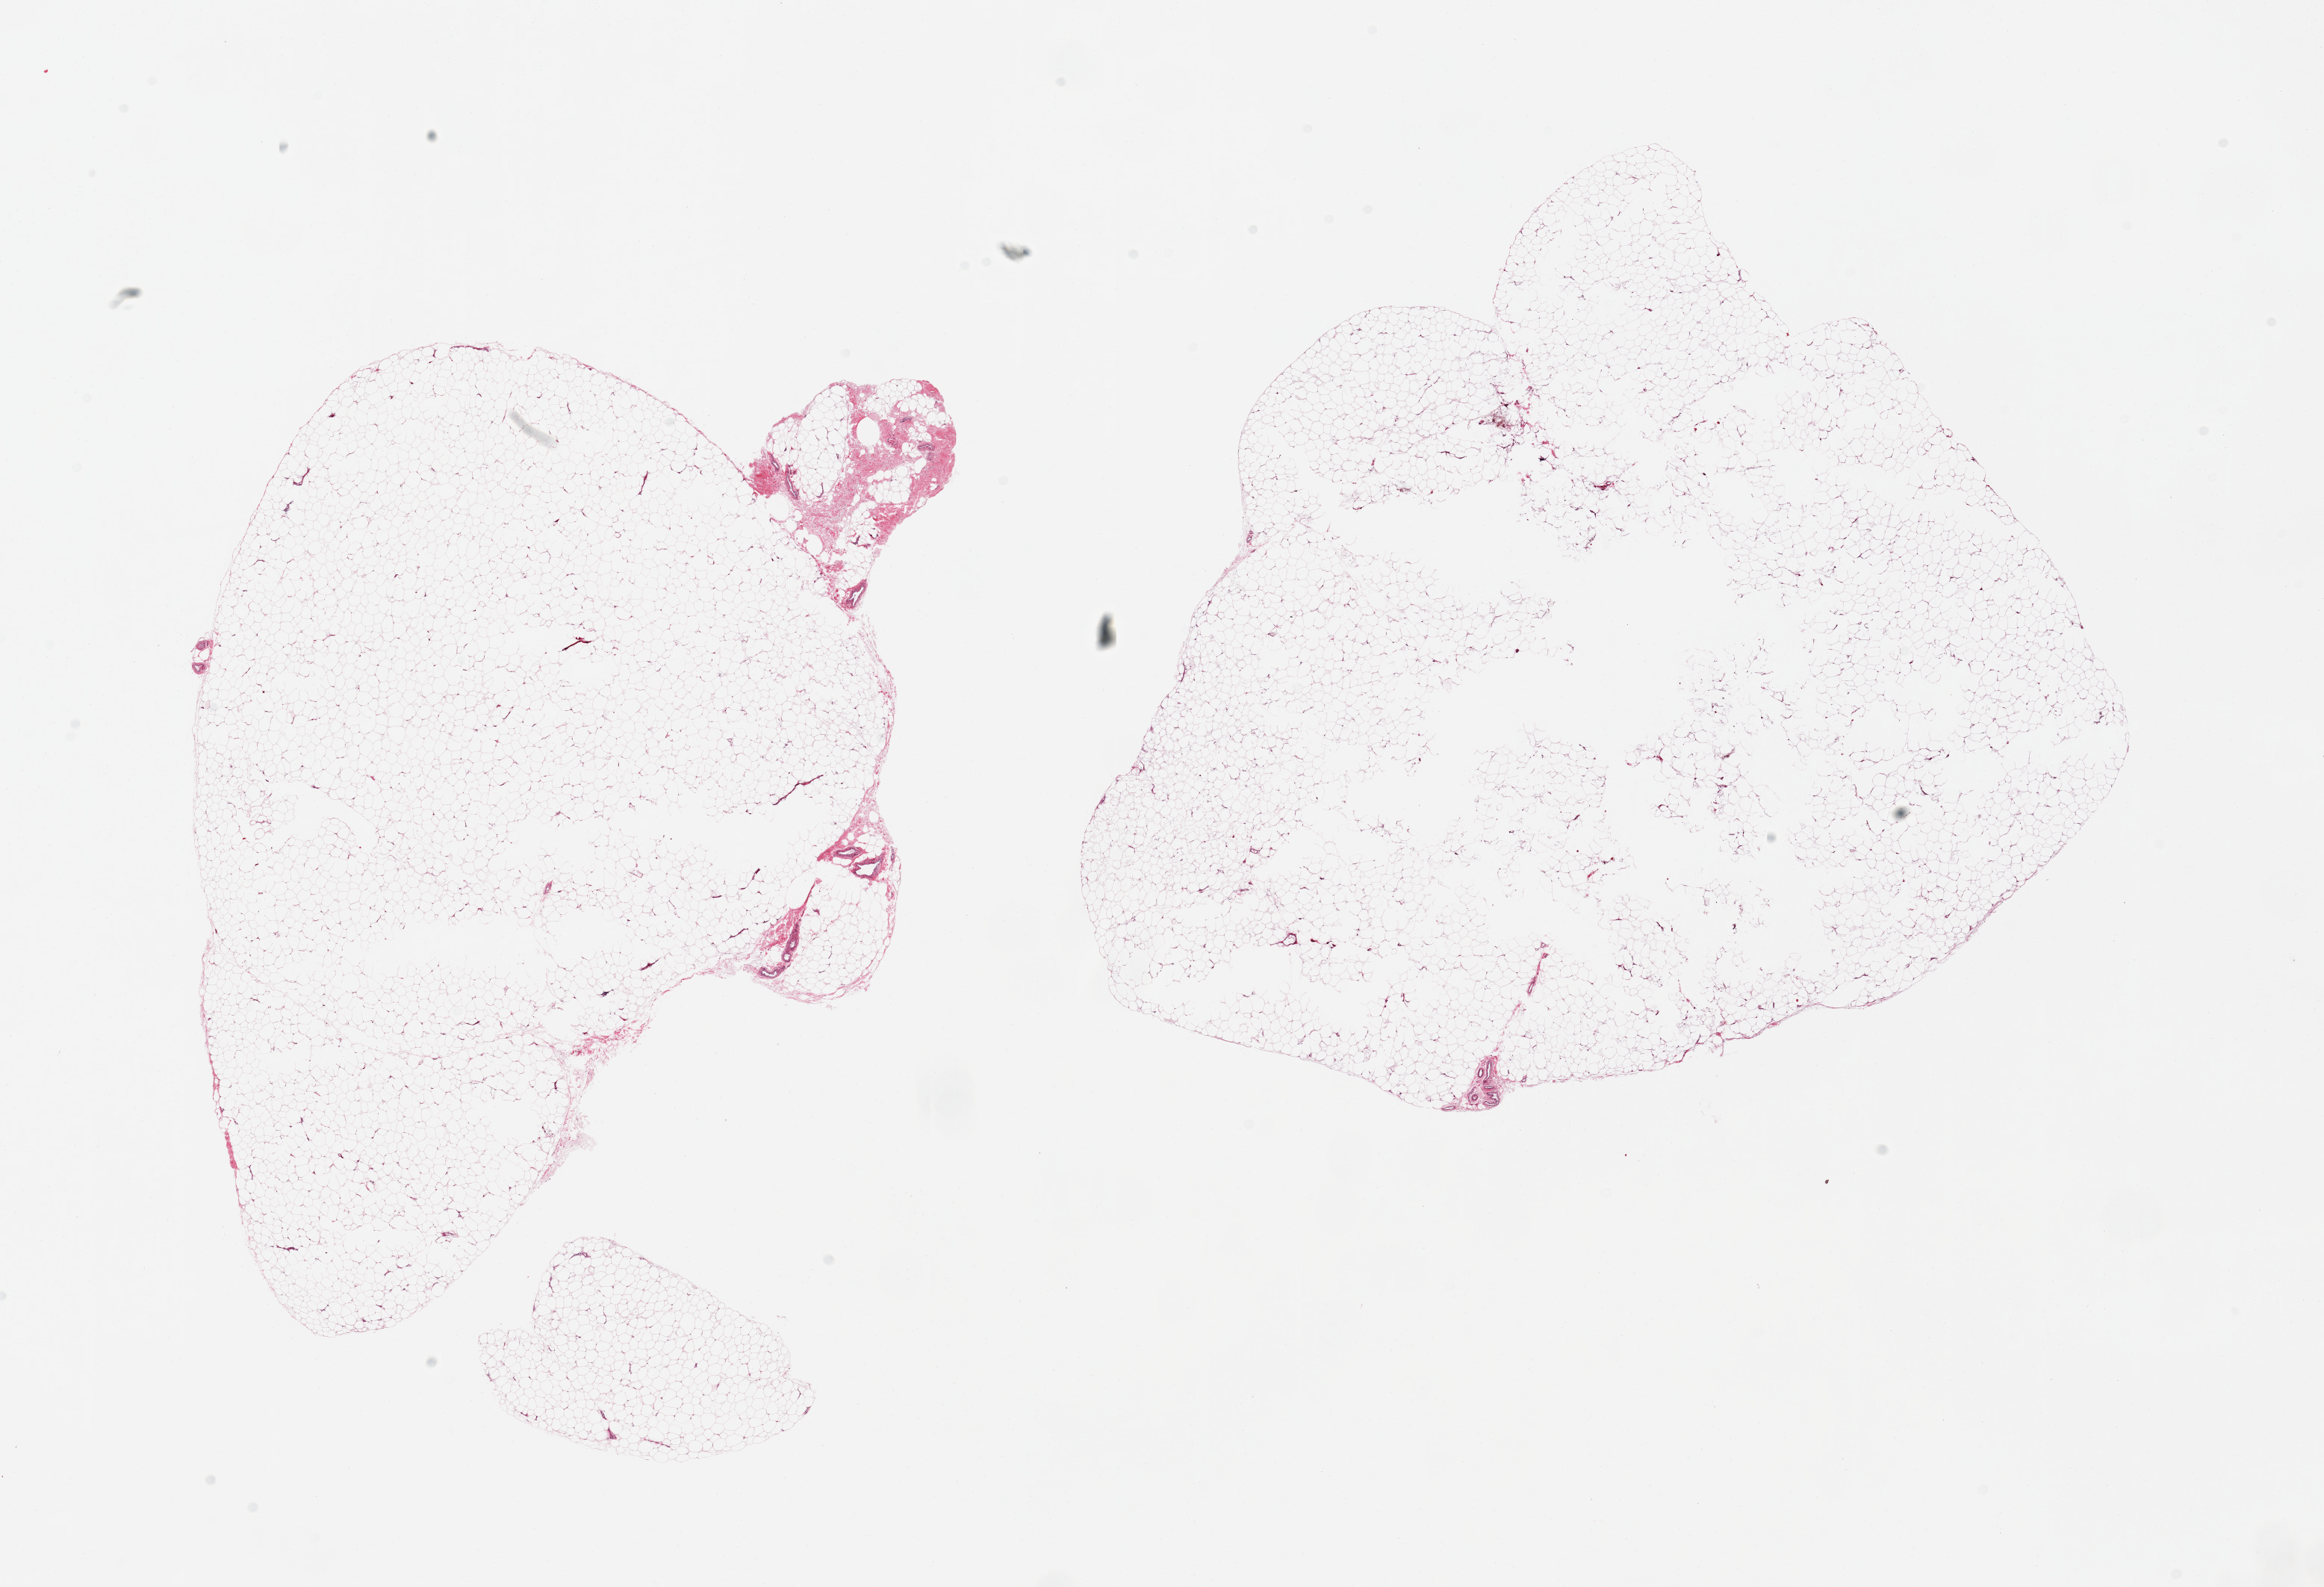
Whole-slide image, hematoxylin and eosin (H&E) stain, brightfield, a low-resolution overview of the entire scanned area, about 24.6 x 16.8 mm, PAXgene-fixed paraffin-embedded (PFPE) section, sampled site (target tissue): adipose tissue, tissue donor sample. Donor: male.
Pathologist's review note for this sample: 2 pieces; several internal holes.